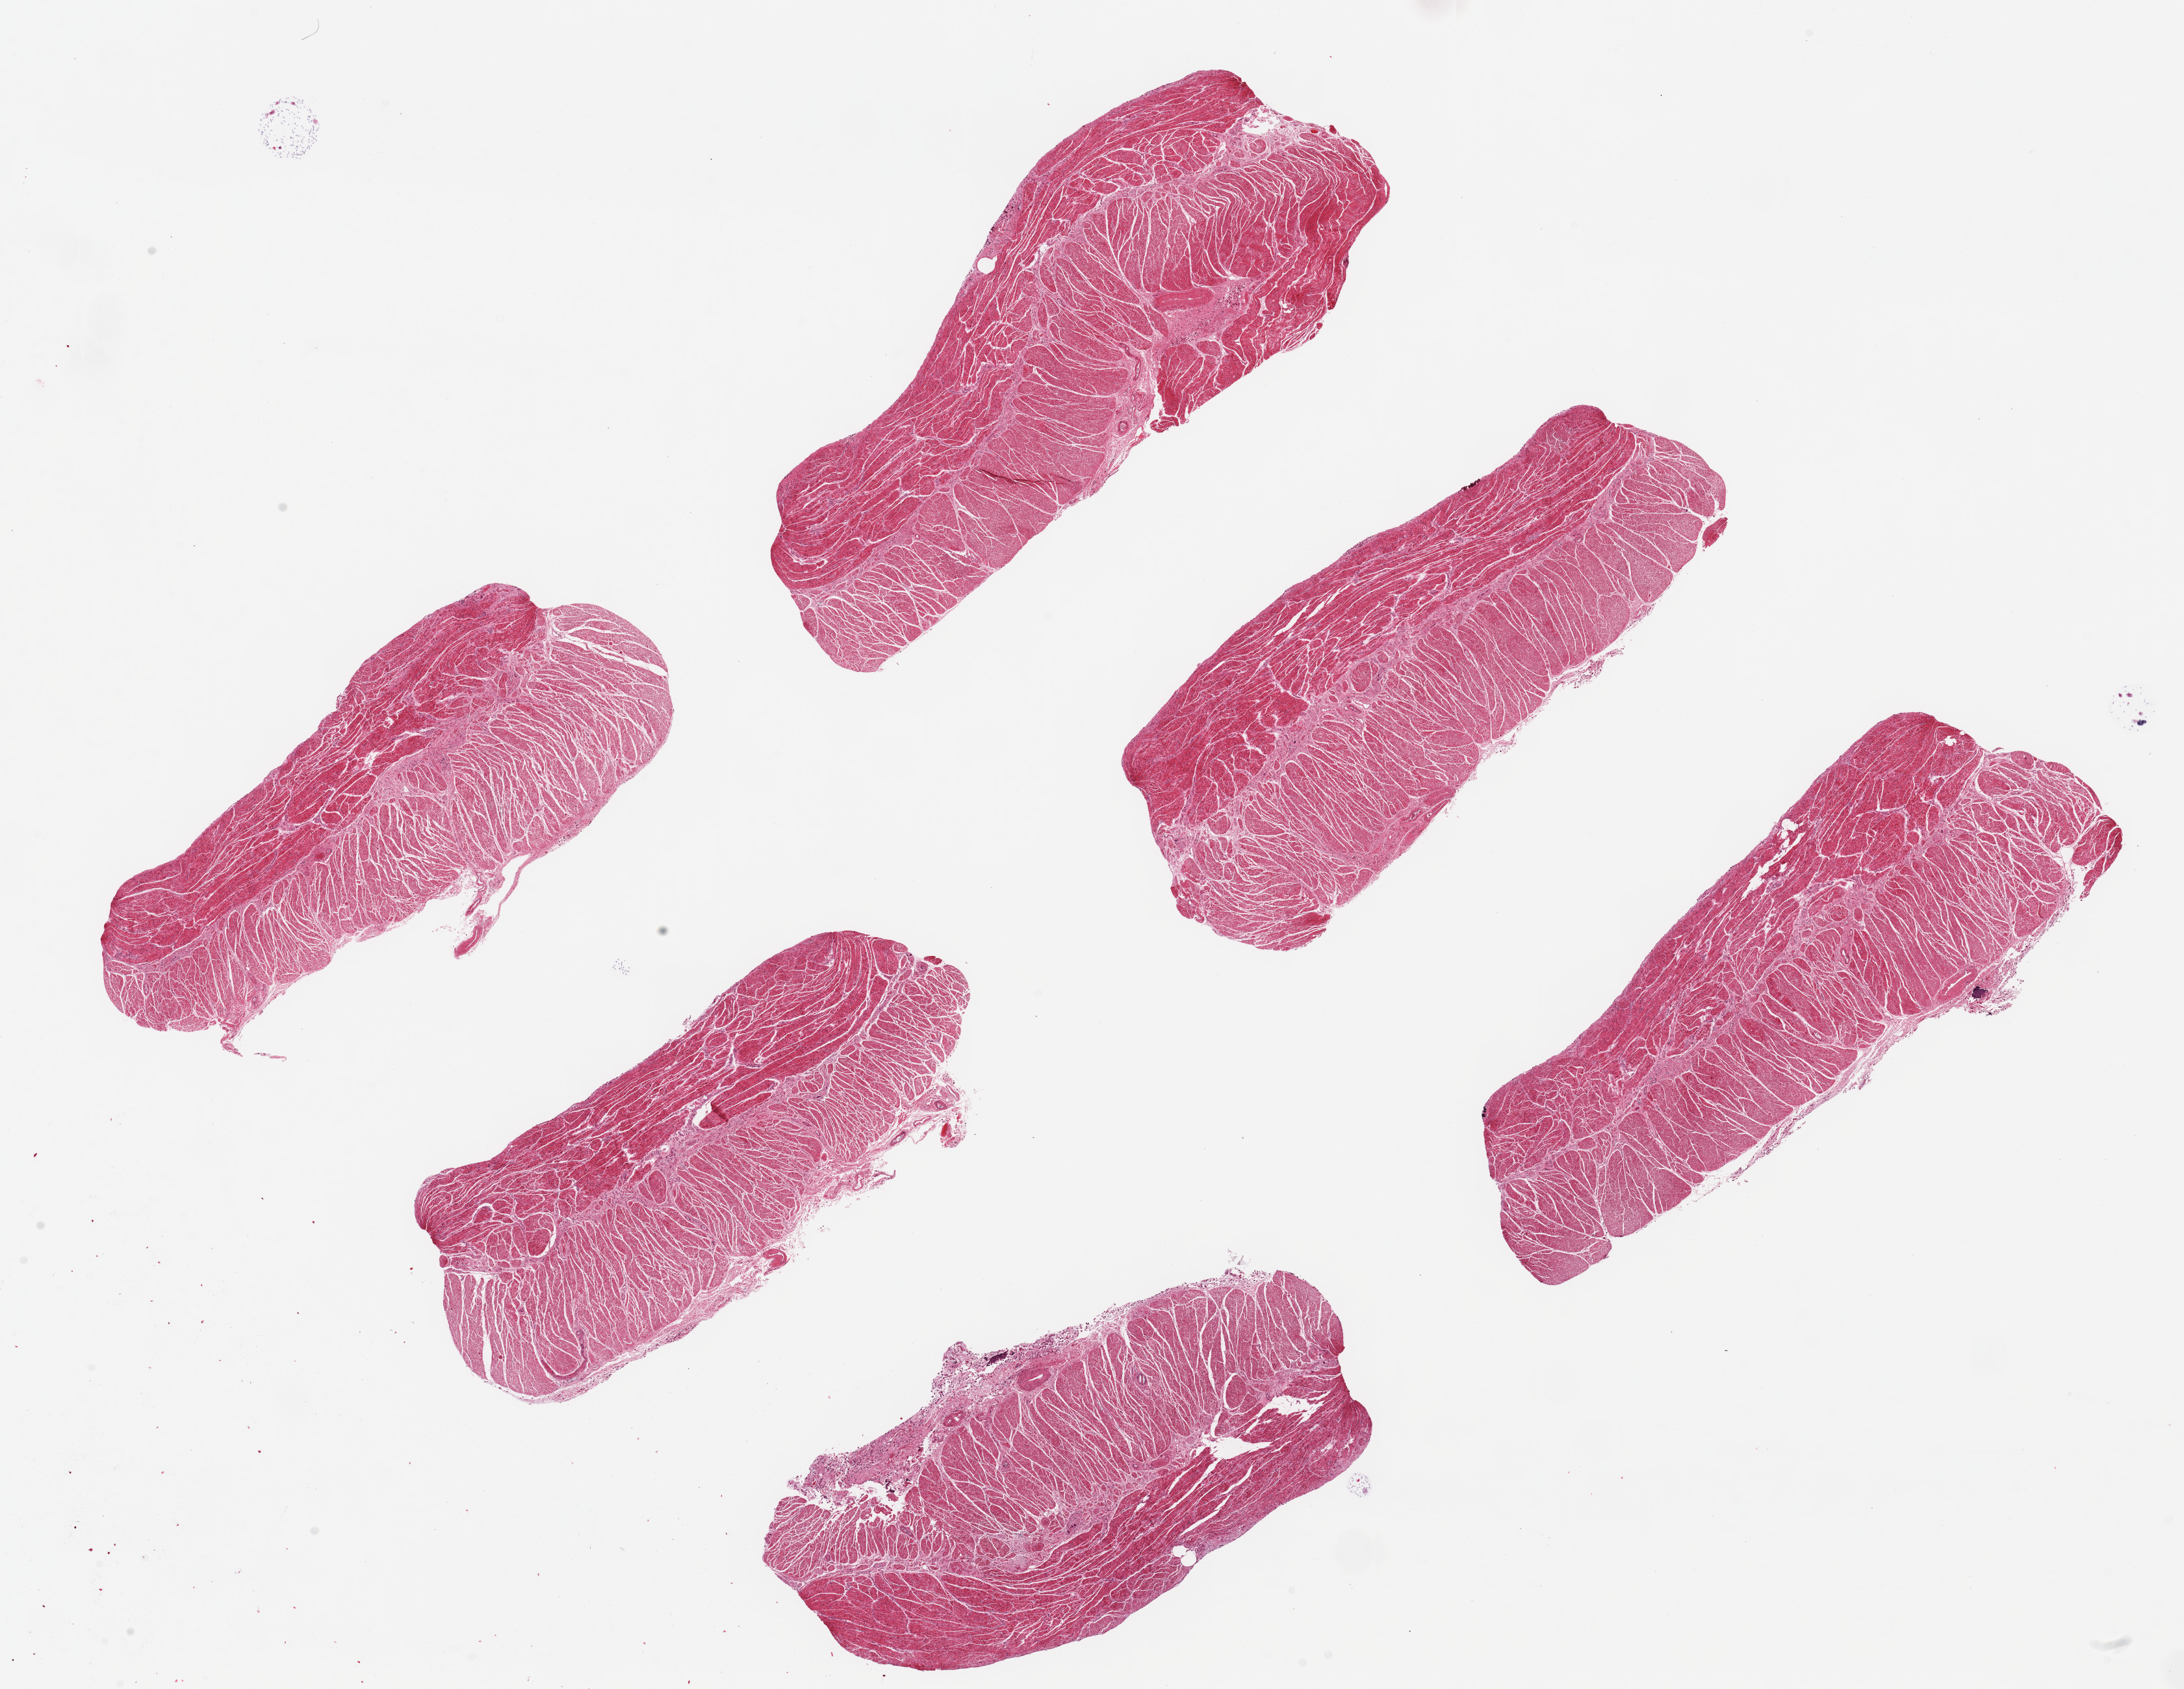
Whole-slide image, H&E stain, low-resolution overview of the scanned area, about 26.6 x 20.6 mm, PAXgene-fixed paraffin-embedded (PFPE) section, target tissue: esophageal muscle, tissue donor sample. Donor sex: female.
Pathologist's review note for this sample: 6 ~8x3mm pieces. Clean specimens.